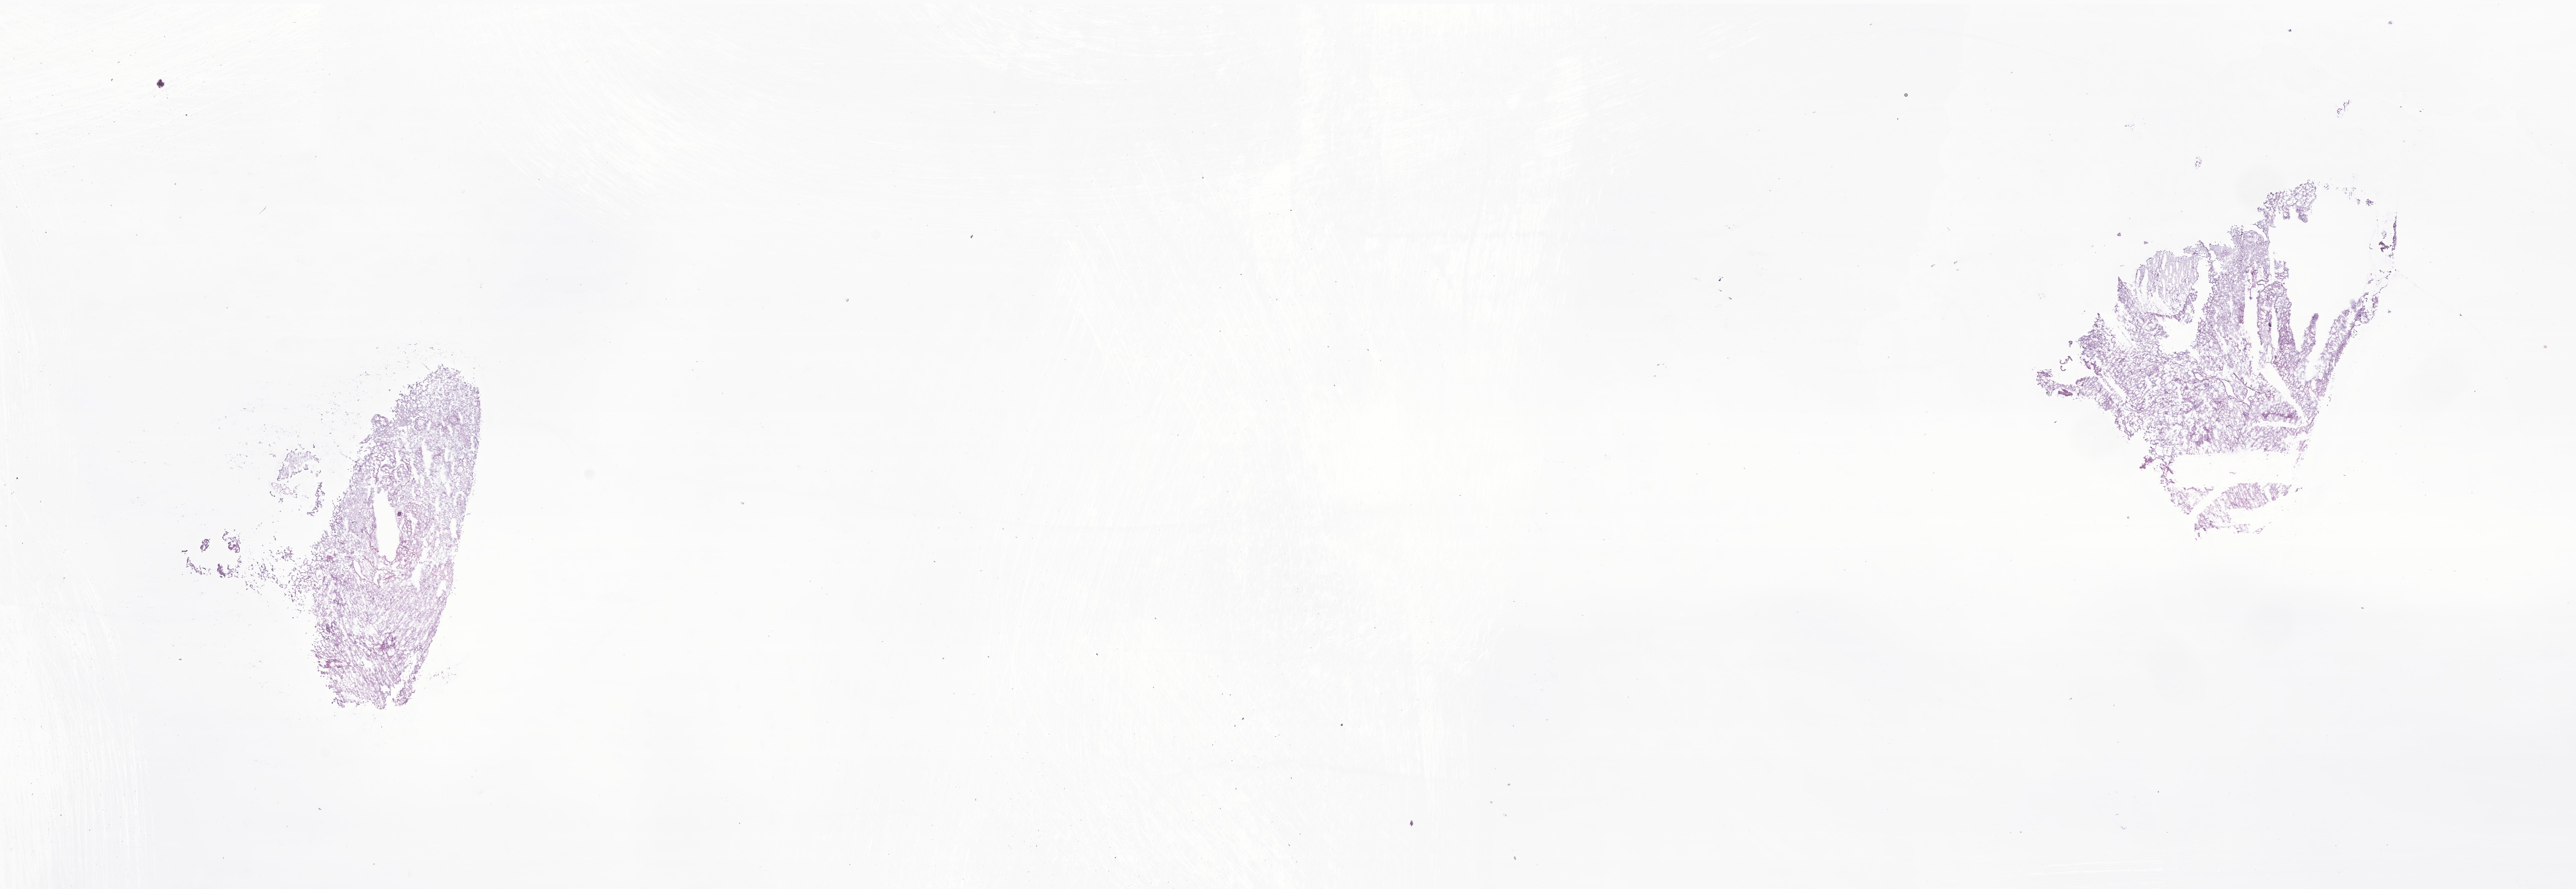
Whole-slide image, H&E stain of tumor tissue from the brain — low-resolution overview of the scanned area, about 26.3 x 9.1 mm. Cryosection (OCT / tissue freezing medium). Patient: male, age 83 months (6 years 11 months).
Recorded diagnosis: Pilocytic astrocytoma.